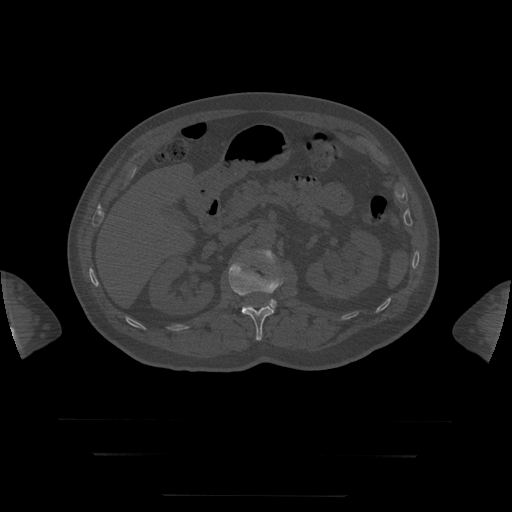
CT including the spine, one axial slice. Position 41 of 397 along the scan axis. Reconstruction kernel STANDARD. 120 kVp. Bone window (W 1800 / L 400 HU). 512 × 512 image matrix, field of view 510 × 510 mm. Patient age 73 years. Case-level facts recorded for this patient, not image findings: primary cancer: prostate.
Outlined on this slice (semi-automatically segmented with operator editing):
- L1 vertebra: bounding box <229,262,283,341> (left, top, right, bottom; pixels)